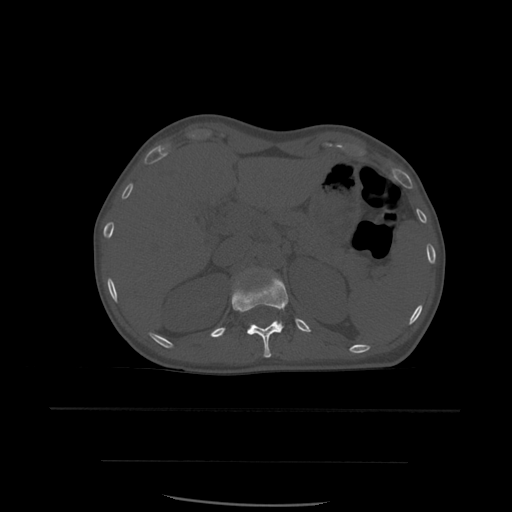
CT including the spine, one axial slice. Slice 270 of 574 in the series (ordered by position). Bone window (W 1800 / L 400 HU). 1.25 mm slice thickness. 512 × 512 image matrix, field of view 392 × 392 mm. Patient age 48 years. Case-level facts recorded for this patient, not image findings: primary cancer: lung; vertebrae with lytic lesions (as recorded): T11.
Structures marked on this image (semi-automatic segmentation, software-assisted and operator-edited):
- T12 vertebra: bounding box <232,275,289,358> (left, top, right, bottom; pixels)